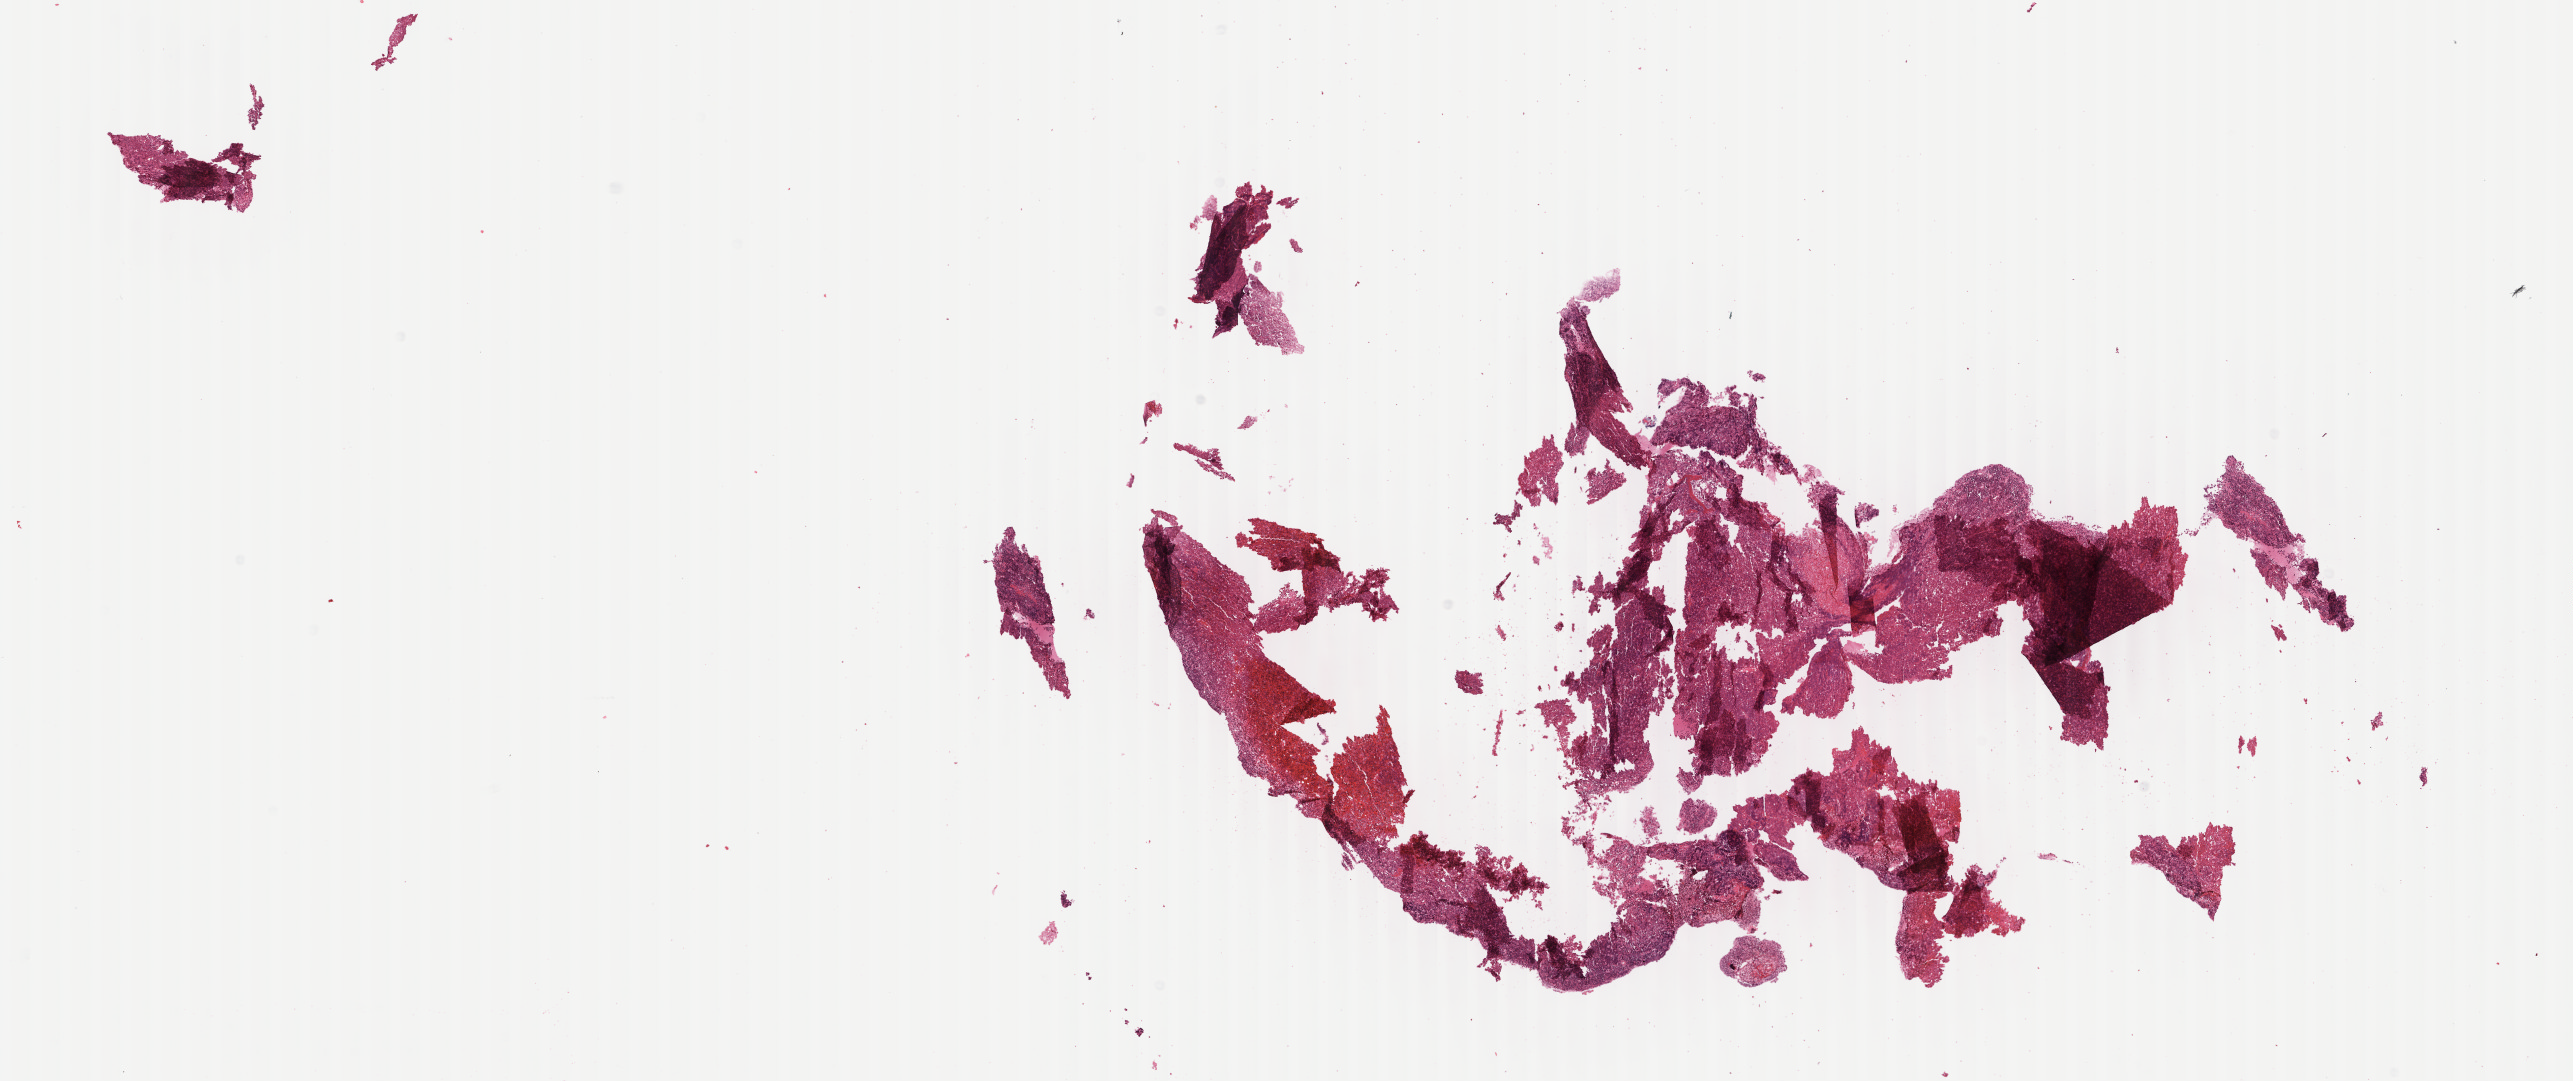
H&E whole-slide image, whole scanned area (about 20.5 x 8.6 mm) shown as a low-resolution overview, formalin-fixed, paraffin-embedded (FFPE) tissue, specimen: primary tumor, site: cranium. Patient female; aged 10. Composition of this section per pathologist review: tumor cells 10%, tumor nuclei 95%, stromal cells 5%, necrosis 85%, normal cells 0%. Infiltration values recorded for this section: lymphocyte infiltration 5%, monocyte infiltration 10%, neutrophil infiltration 5%.
- histologic diagnosis: Burkitt lymphoma, NOS
- Ann Arbor stage (patient): Stage I
- section: bottom of the tissue portion